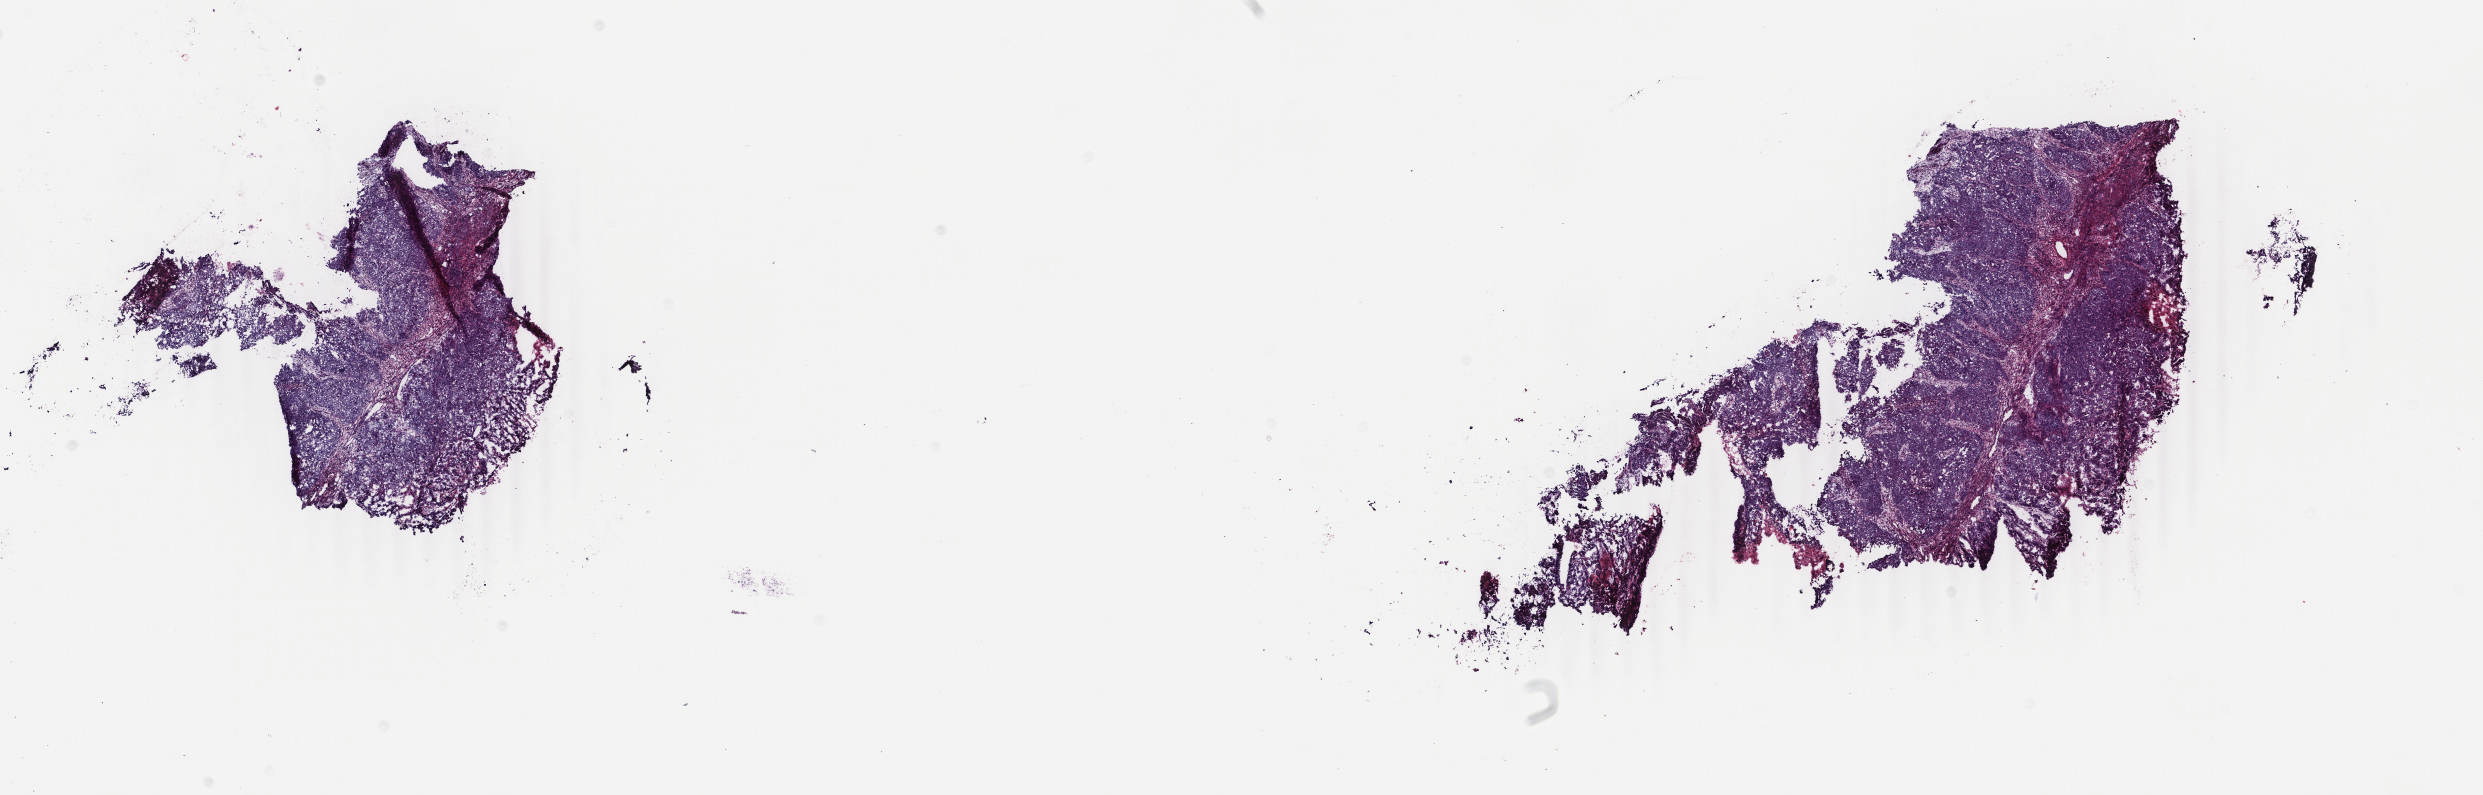
Digitized H&E-stained tissue section (whole slide) — shown as a low-resolution overview of the whole scanned area (about 19.8 x 6.3 mm, slide scanned at 40x), frozen section from the top of the tissue portion, primary tumour sample from the uterus. Female patient; age at initial diagnosis 73 years. Histologic grade: G3 (poorly differentiated). Pathologist review of this section (percent, as recorded): tumour cells 70%, tumour nuclei 80%, normal cells 20%, stromal cells 0%, necrosis 10%. Infiltration values recorded for this section: lymphocyte infiltration 10%, monocyte infiltration 0%, neutrophil infiltration 0%.
FIGO stage: IIIC2. Histologic diagnosis: Serous cystadenocarcinoma, NOS (endometrium). Lymph nodes positive (case pathology): 3 of 5 examined.